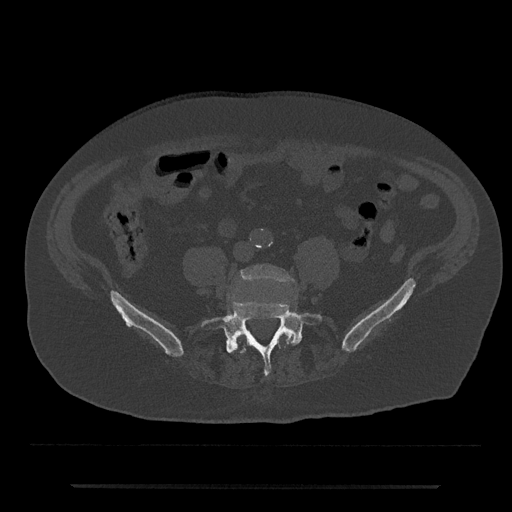
CT including the spine, one axial slice; position 305 of 797 along the scan axis; bone window (W 1800 / L 400 HU); 0.5 mm slice thickness; 512 × 512 image matrix, field of view 434 × 434 mm. Male patient, age 80 years. From the clinical record (not read from this slice): primary cancer: prostate; vertebrae with lytic lesions (as recorded): L1, T11.
Outlined on this slice (semi-automatic segmentation, software-assisted and operator-edited):
- L4 vertebra: bounding box [x1, y1, x2, y2] px = [240, 265, 295, 341]
- L5 vertebra: [201, 300, 323, 376]